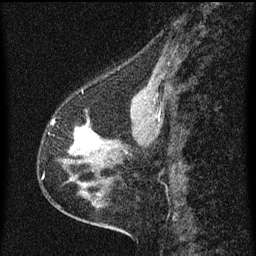
Breast MRI (dynamic contrast-enhanced), one sagittal slice. Position 26 of 60 along the scan axis. Dynamic contrast-enhanced series, image 2 of 3 at this slice position (ordered by acquisition). 1.5 T. TE 4.2 ms, TR 8 ms. 2 mm slice thickness. 256 × 256 image matrix, field of view 180 × 180 mm. Patient: female, 56 years.
Annotated regions visible in this slice (semi-automatic segmentation, software-assisted and operator-edited):
- analysis volume of interest (the breast-tissue region the enhancement analysis was run in; not a lesion): bounding box <65,114,102,181> (left, top, right, bottom; pixels)
- tumour enhancement mask (voxels above the 70 % enhancement threshold inside the analysis volume of interest): <75,125,97,149>